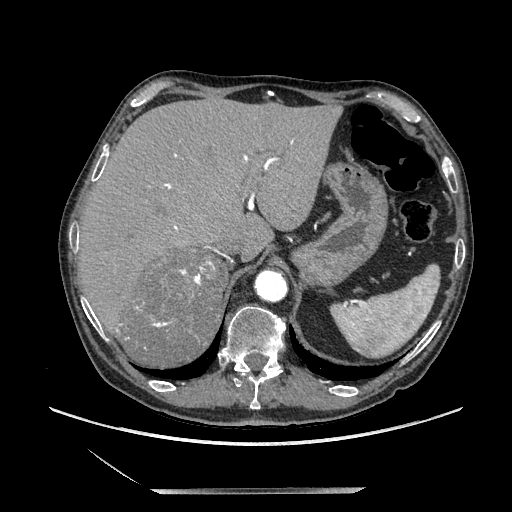
Contrast-enhanced abdominal CT, one axial slice; slice 162 of 243 in the series (ordered by position); soft-tissue window (W 400 / L 40 HU); 1.25 mm slice thickness; 512 × 512 image matrix, field of view 420 × 420 mm. Male patient. Case-level facts recorded for this patient, not image findings: diagnosis: adrenocortical carcinoma; tumour side: right adrenal; tumour size at pathology: 16 cm; Ki-67 index: 17 %; stage (as recorded): 3.
Structures marked on this image (semi-automatic segmentation, software-assisted and operator-edited):
- mass: bounding box <123,252,226,370> (left, top, right, bottom; pixels)